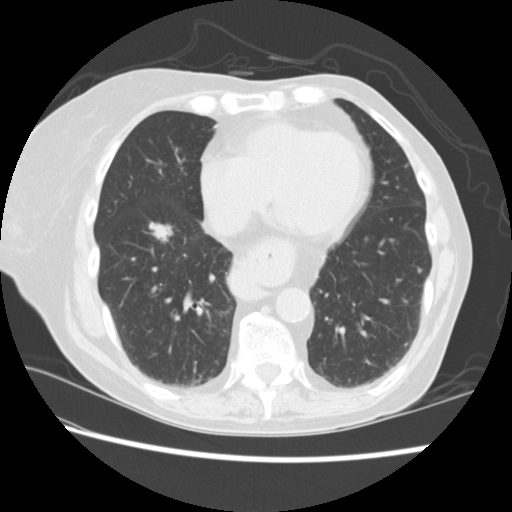
Low-dose screening chest CT, one axial slice. Reconstruction kernel STANDARD. Lung window (W 1500 / L -600 HU). 2.5 mm slice thickness. 512 × 512 image matrix, field of view 340 × 340 mm.
Structures marked on this image (expert manual segmentation):
- lesion 2 (tumor, lower lobe of right lung): bounding box [x1, y1, x2, y2] px = [149, 223, 172, 242]